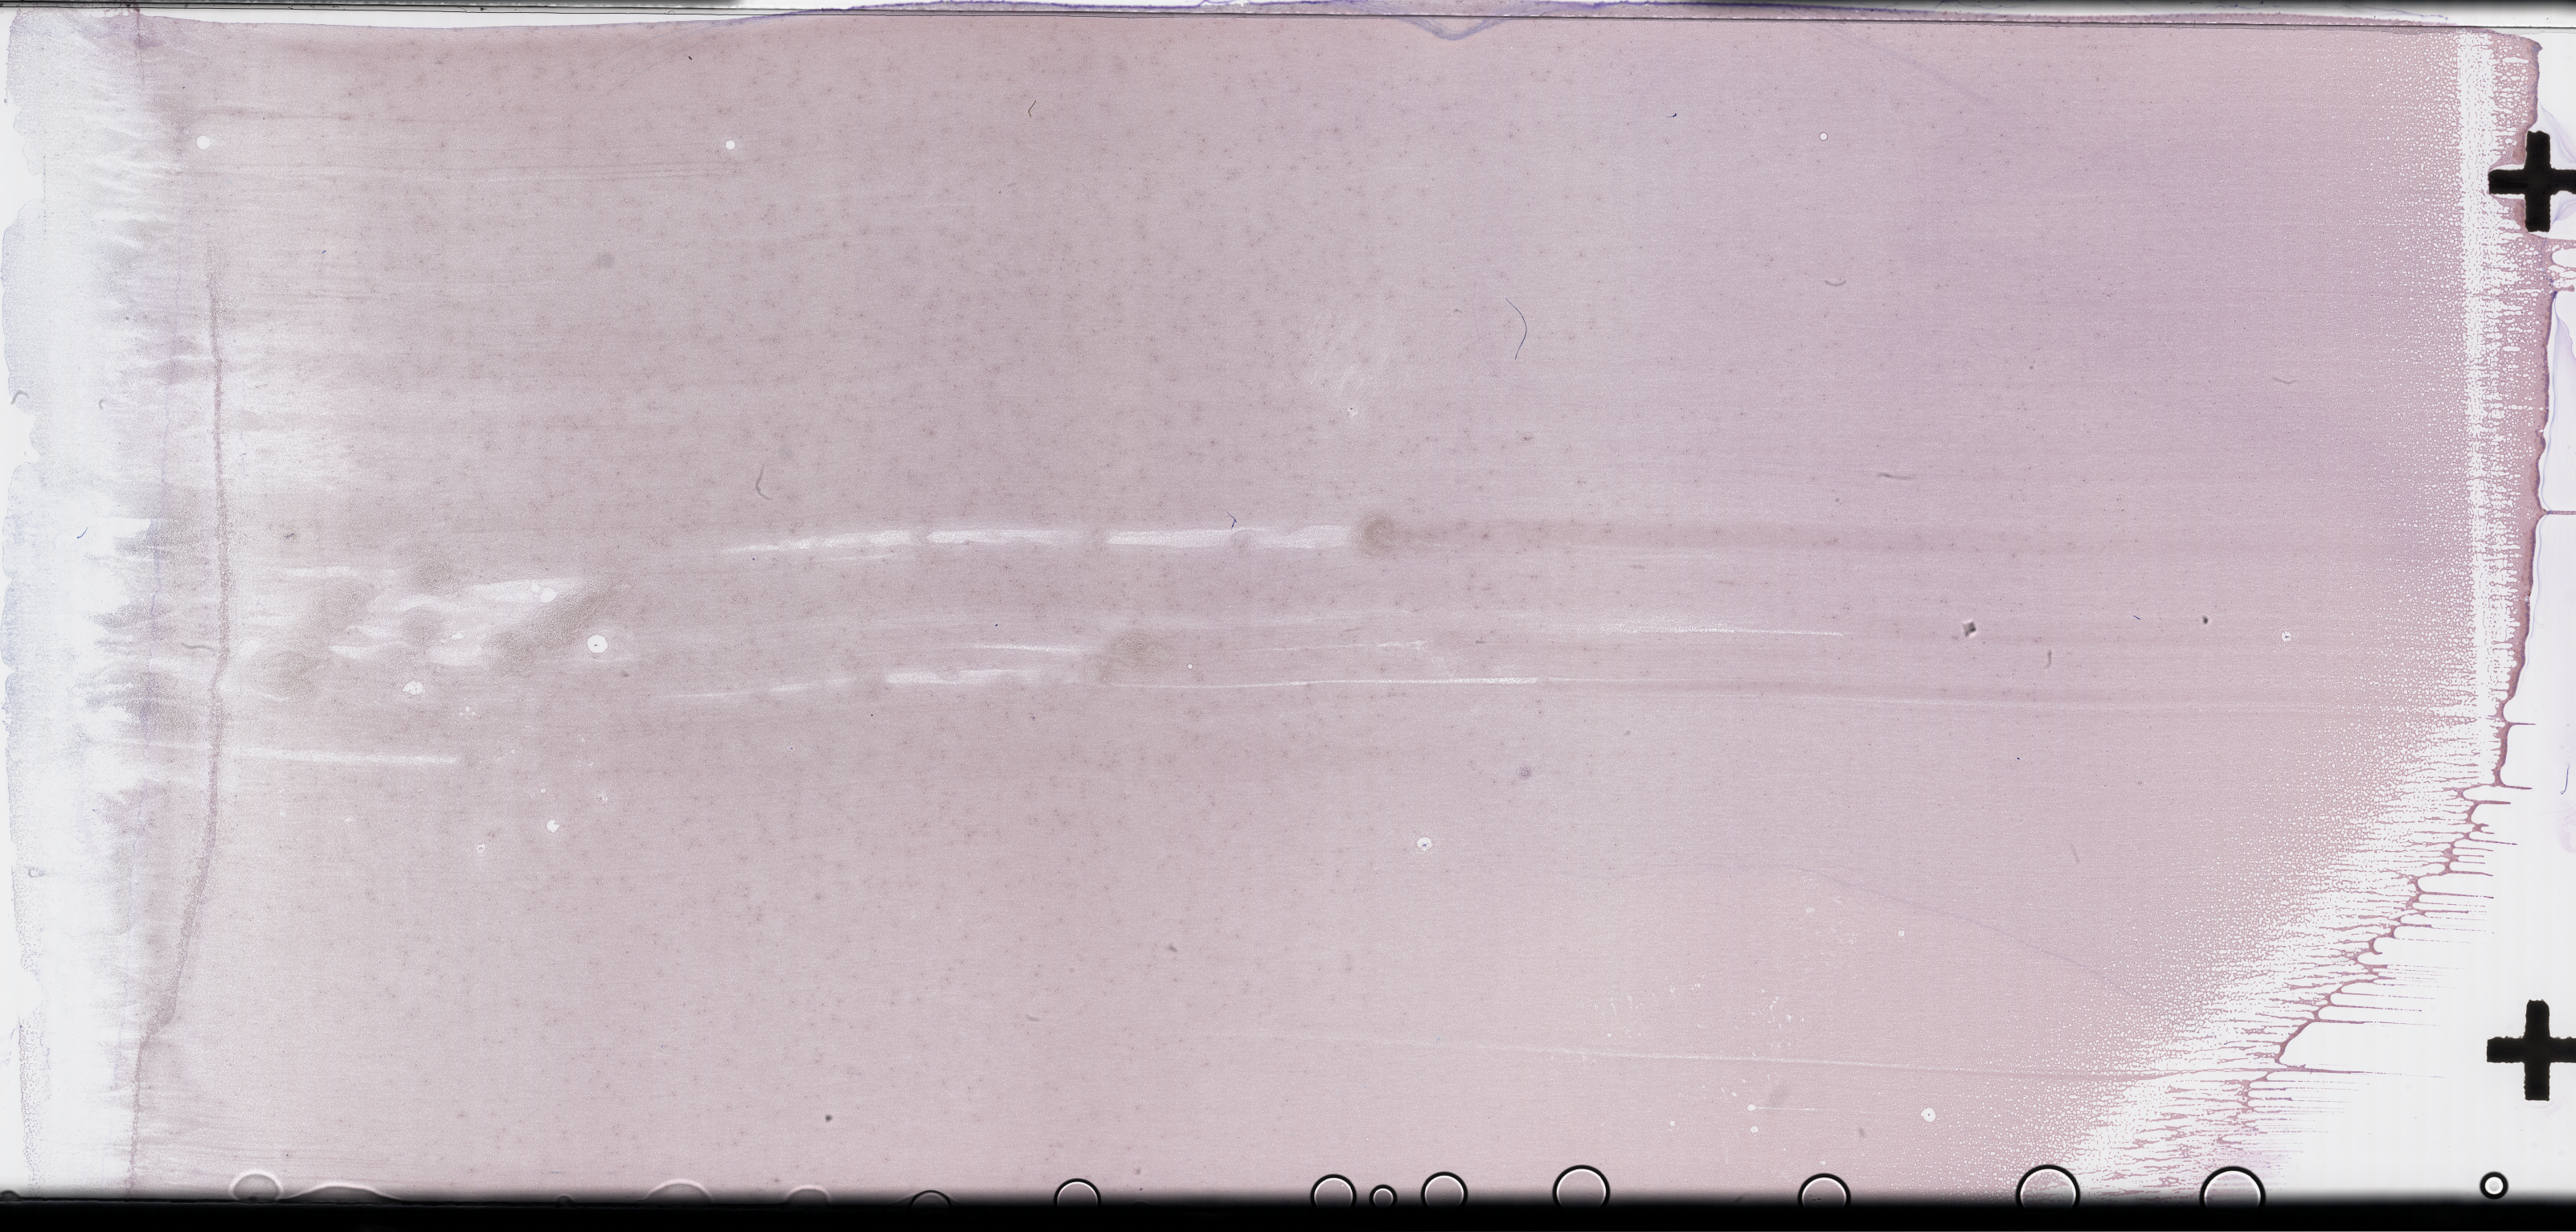
Whole-slide image of a whole blood smear, Wright–Giemsa stain — low-resolution overview of the scanned area, about 51.8 x 24.8 mm. Specimen time point: collected on treatment. Patient: male.
* patient diagnosis: Plasma Cell Myeloma